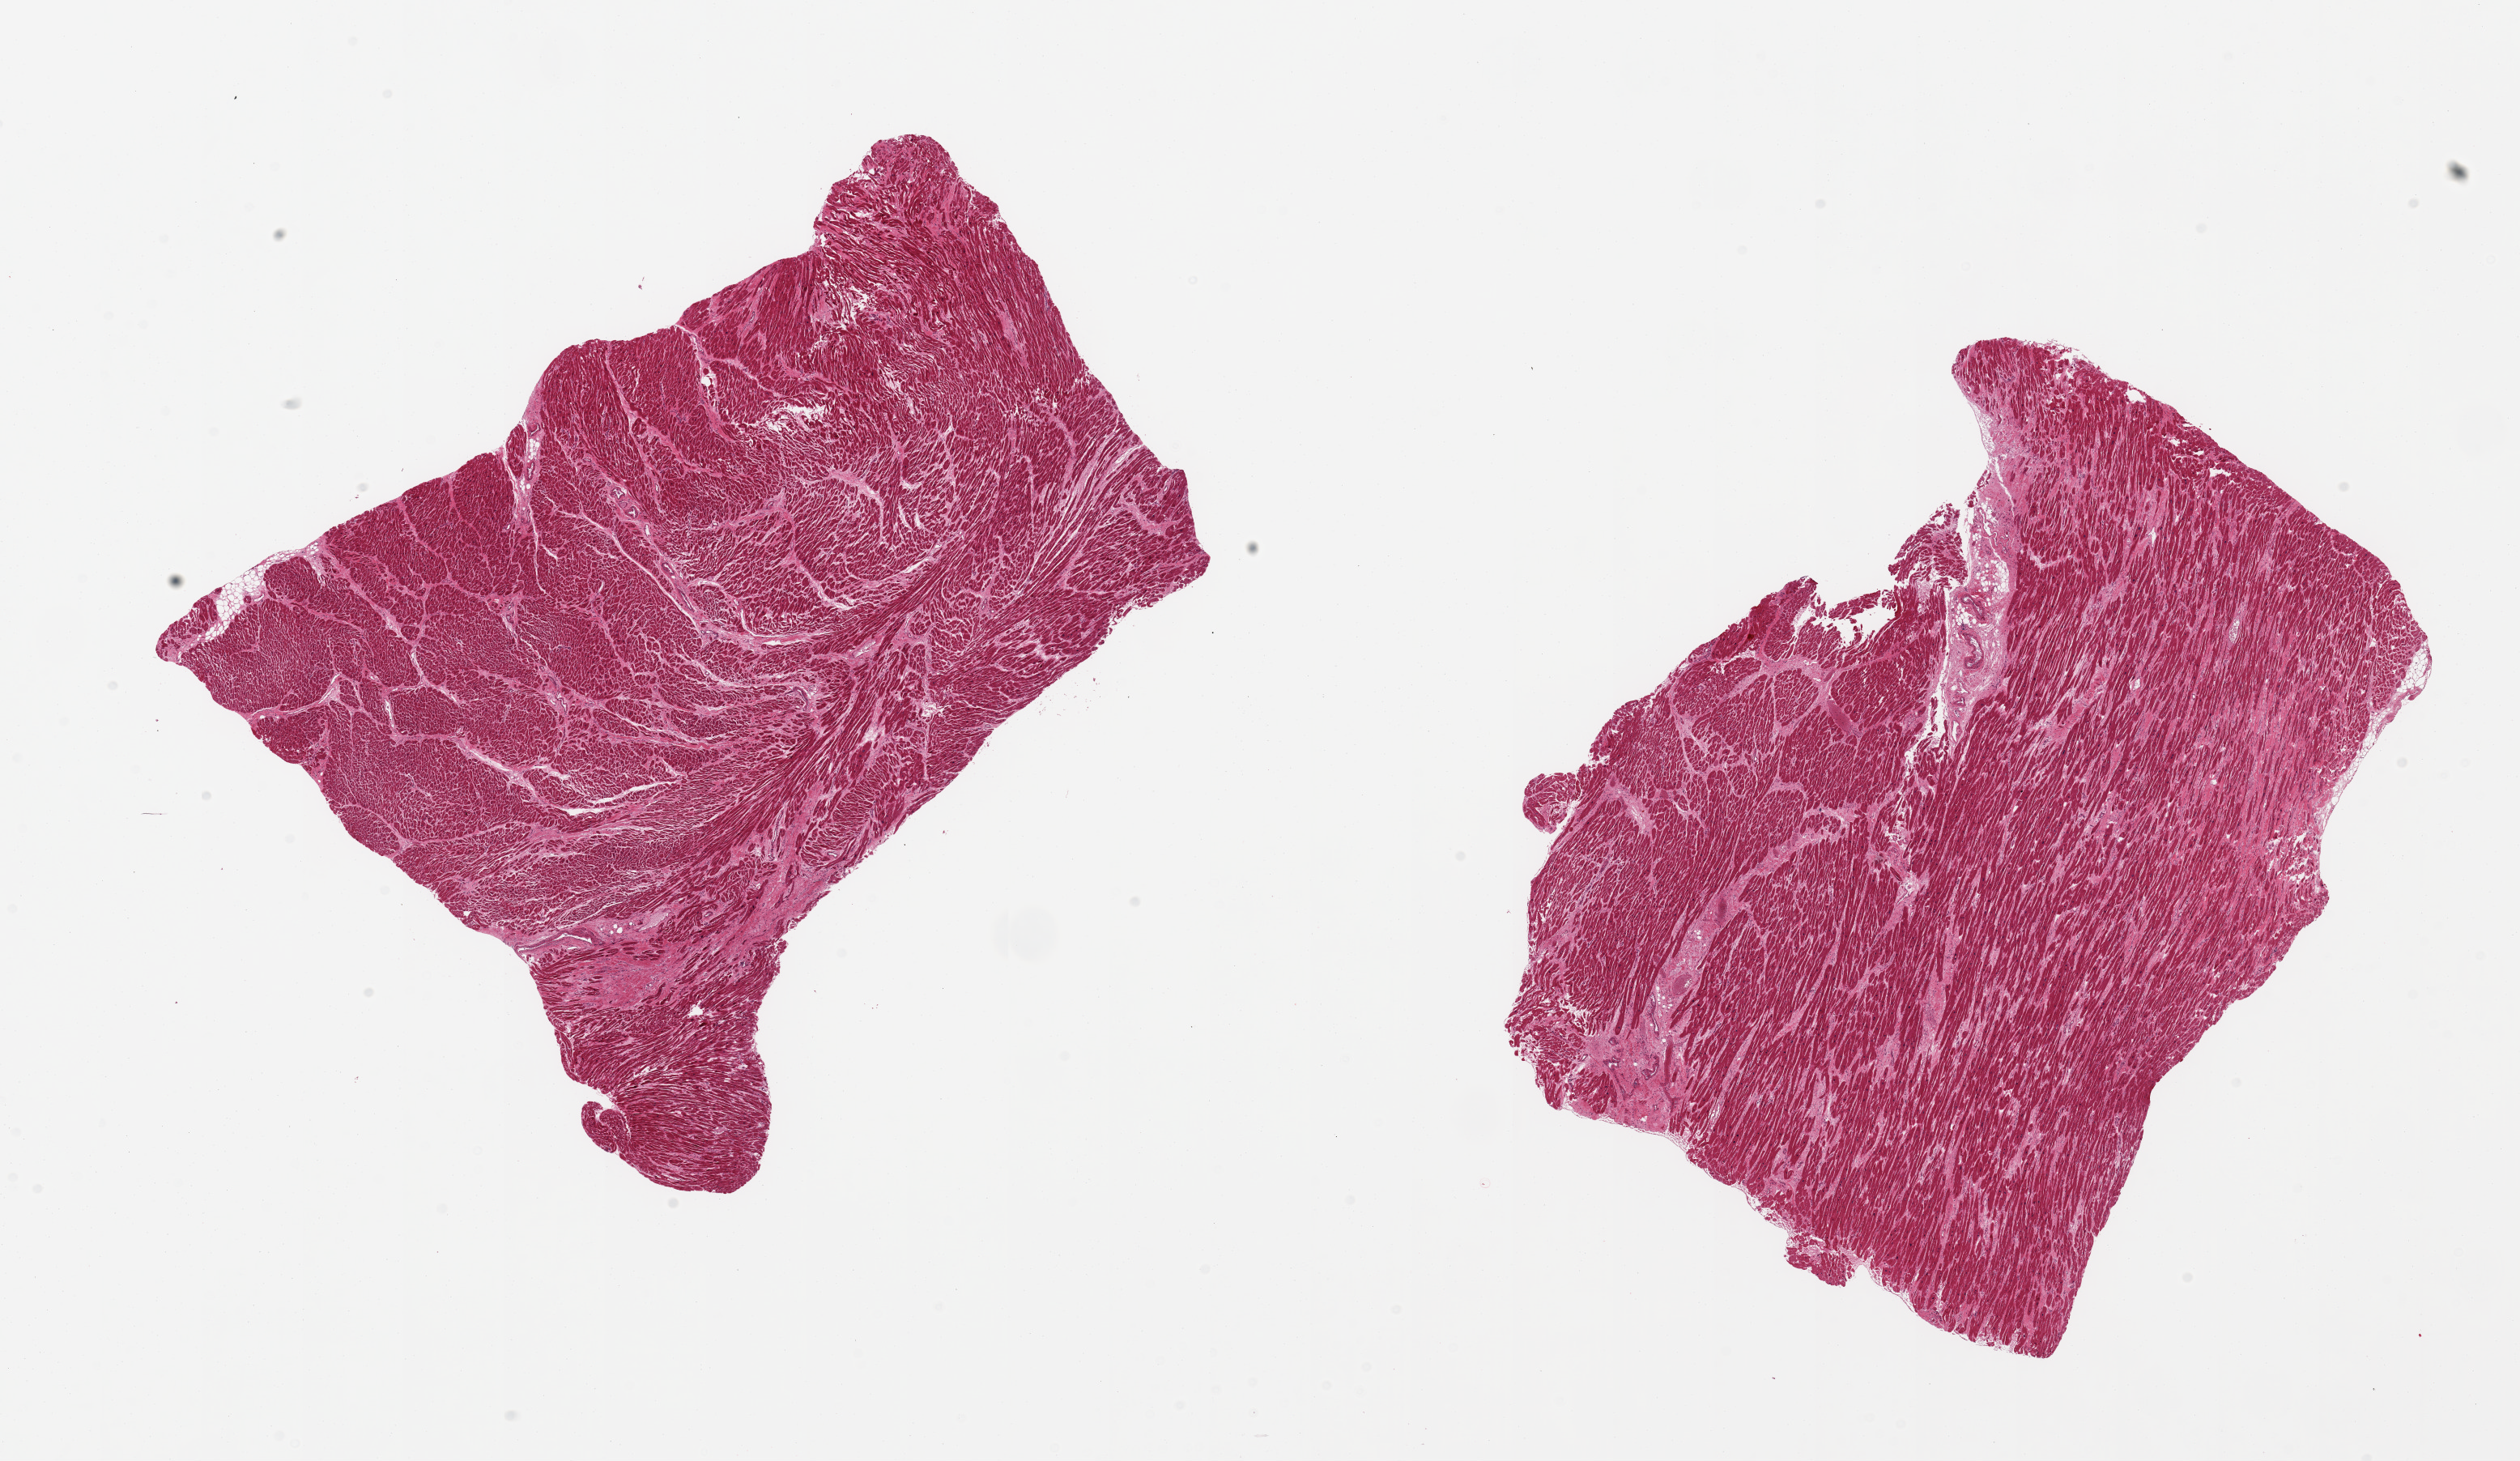
H&E whole-slide image, whole scanned area (about 24.6 x 14.3 mm, acquisition: 20x scan) shown as a low-resolution overview. PAXgene-fixed, paraffin-embedded tissue. Section of heart (target tissue). Tissue donor sample.
- reviewer comment on this tissue sample: 2 pieces, moderate-marked interstitial fibrosis/chronic ischemic damage